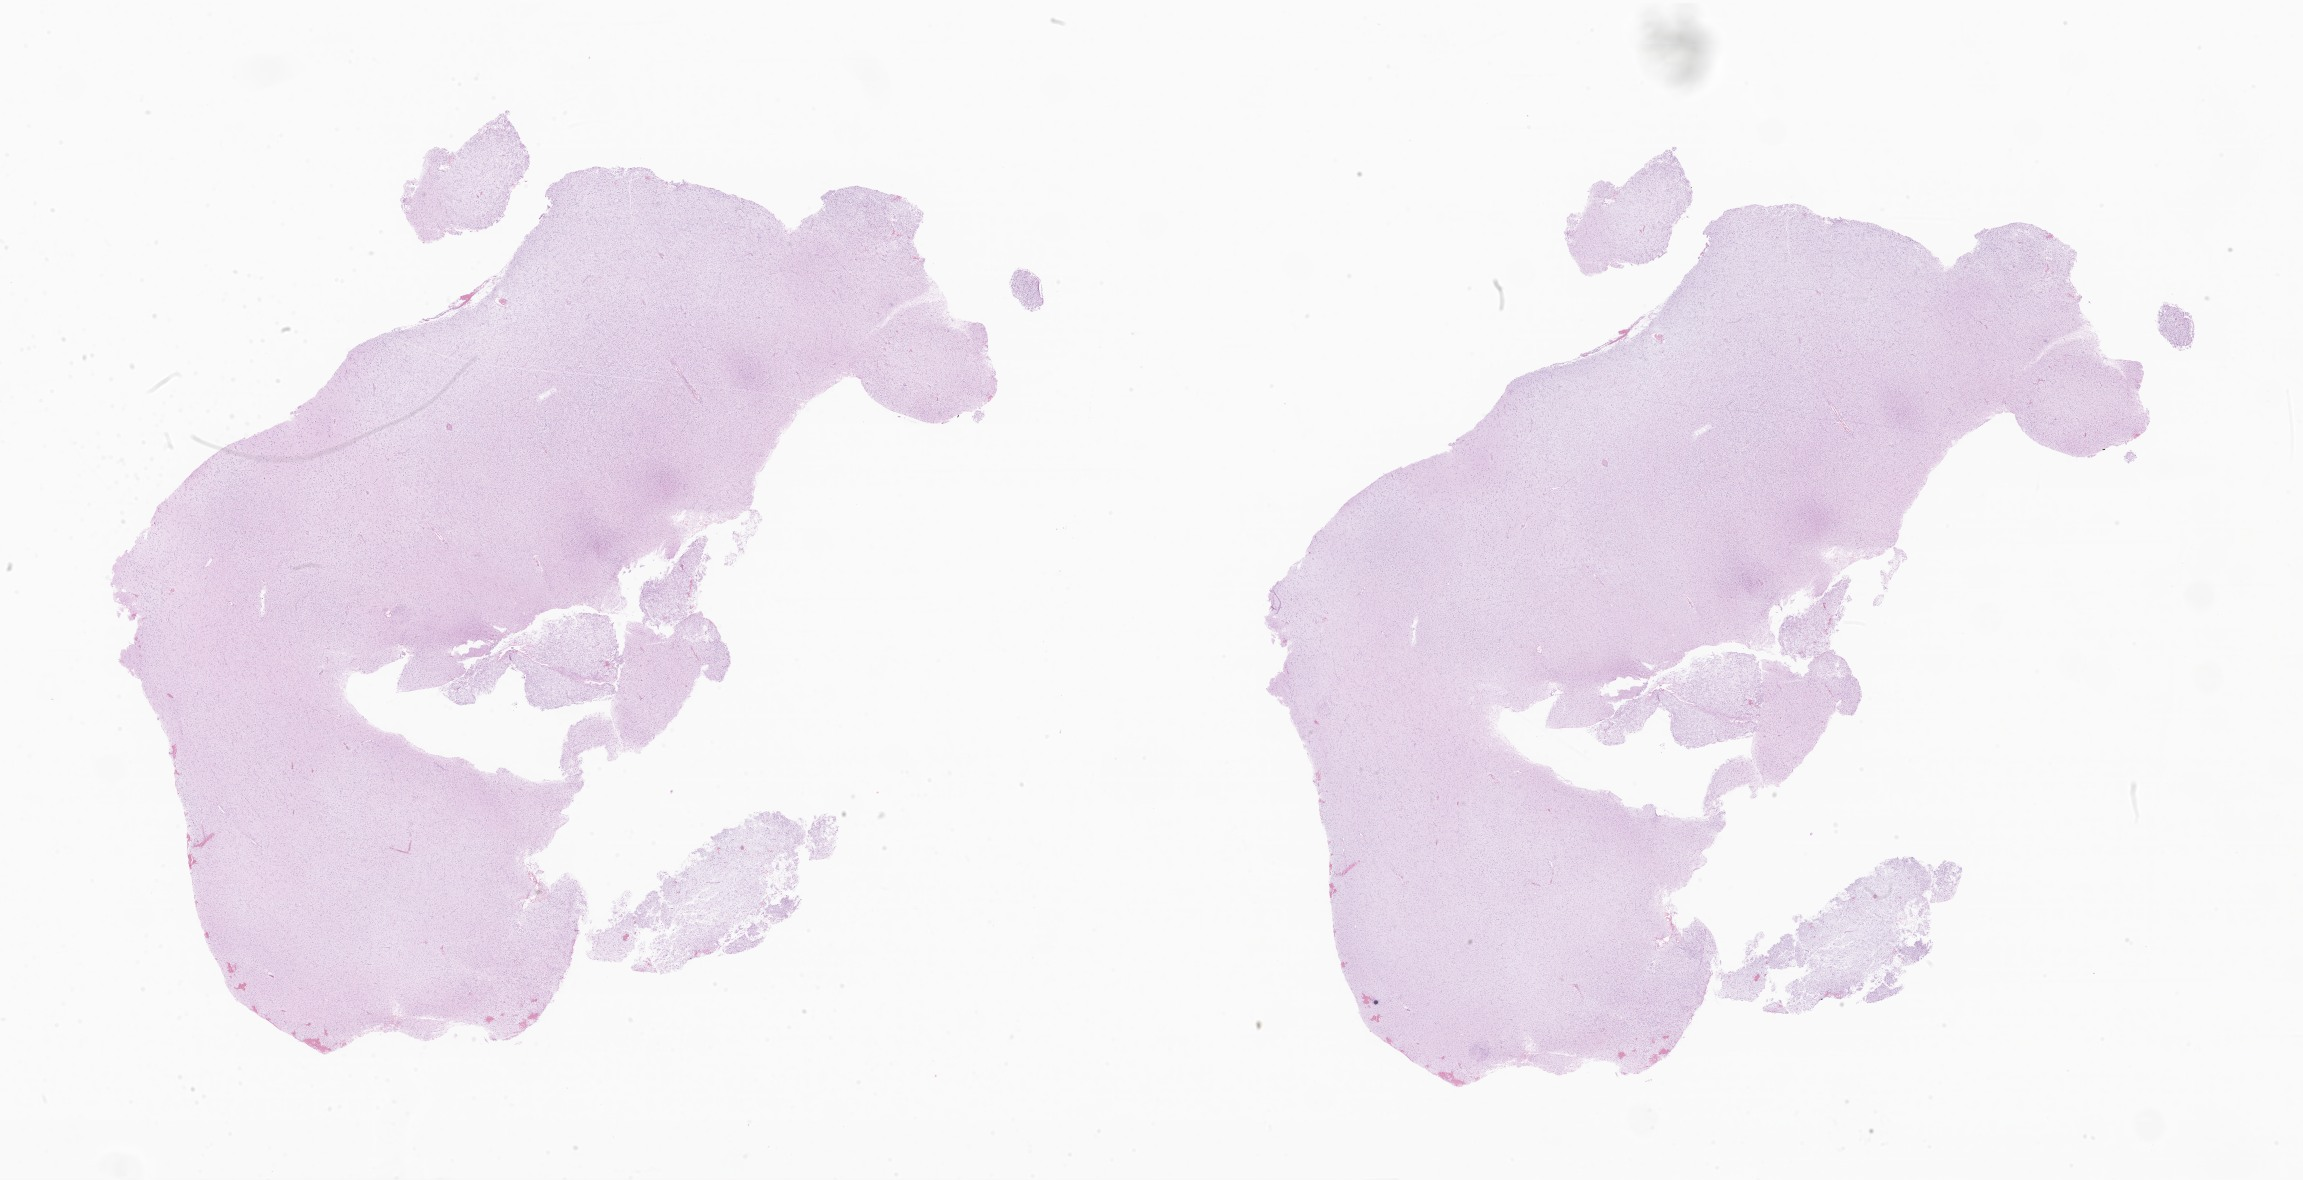
H&E whole-slide image of tumor tissue from the brain, low-resolution overview of the scanned area, about 38.8 x 19.9 mm, formalin-fixed paraffin-embedded section. Male patient, age 43 months (3 years 7 months).
Diagnosis: Pilocytic astrocytoma.